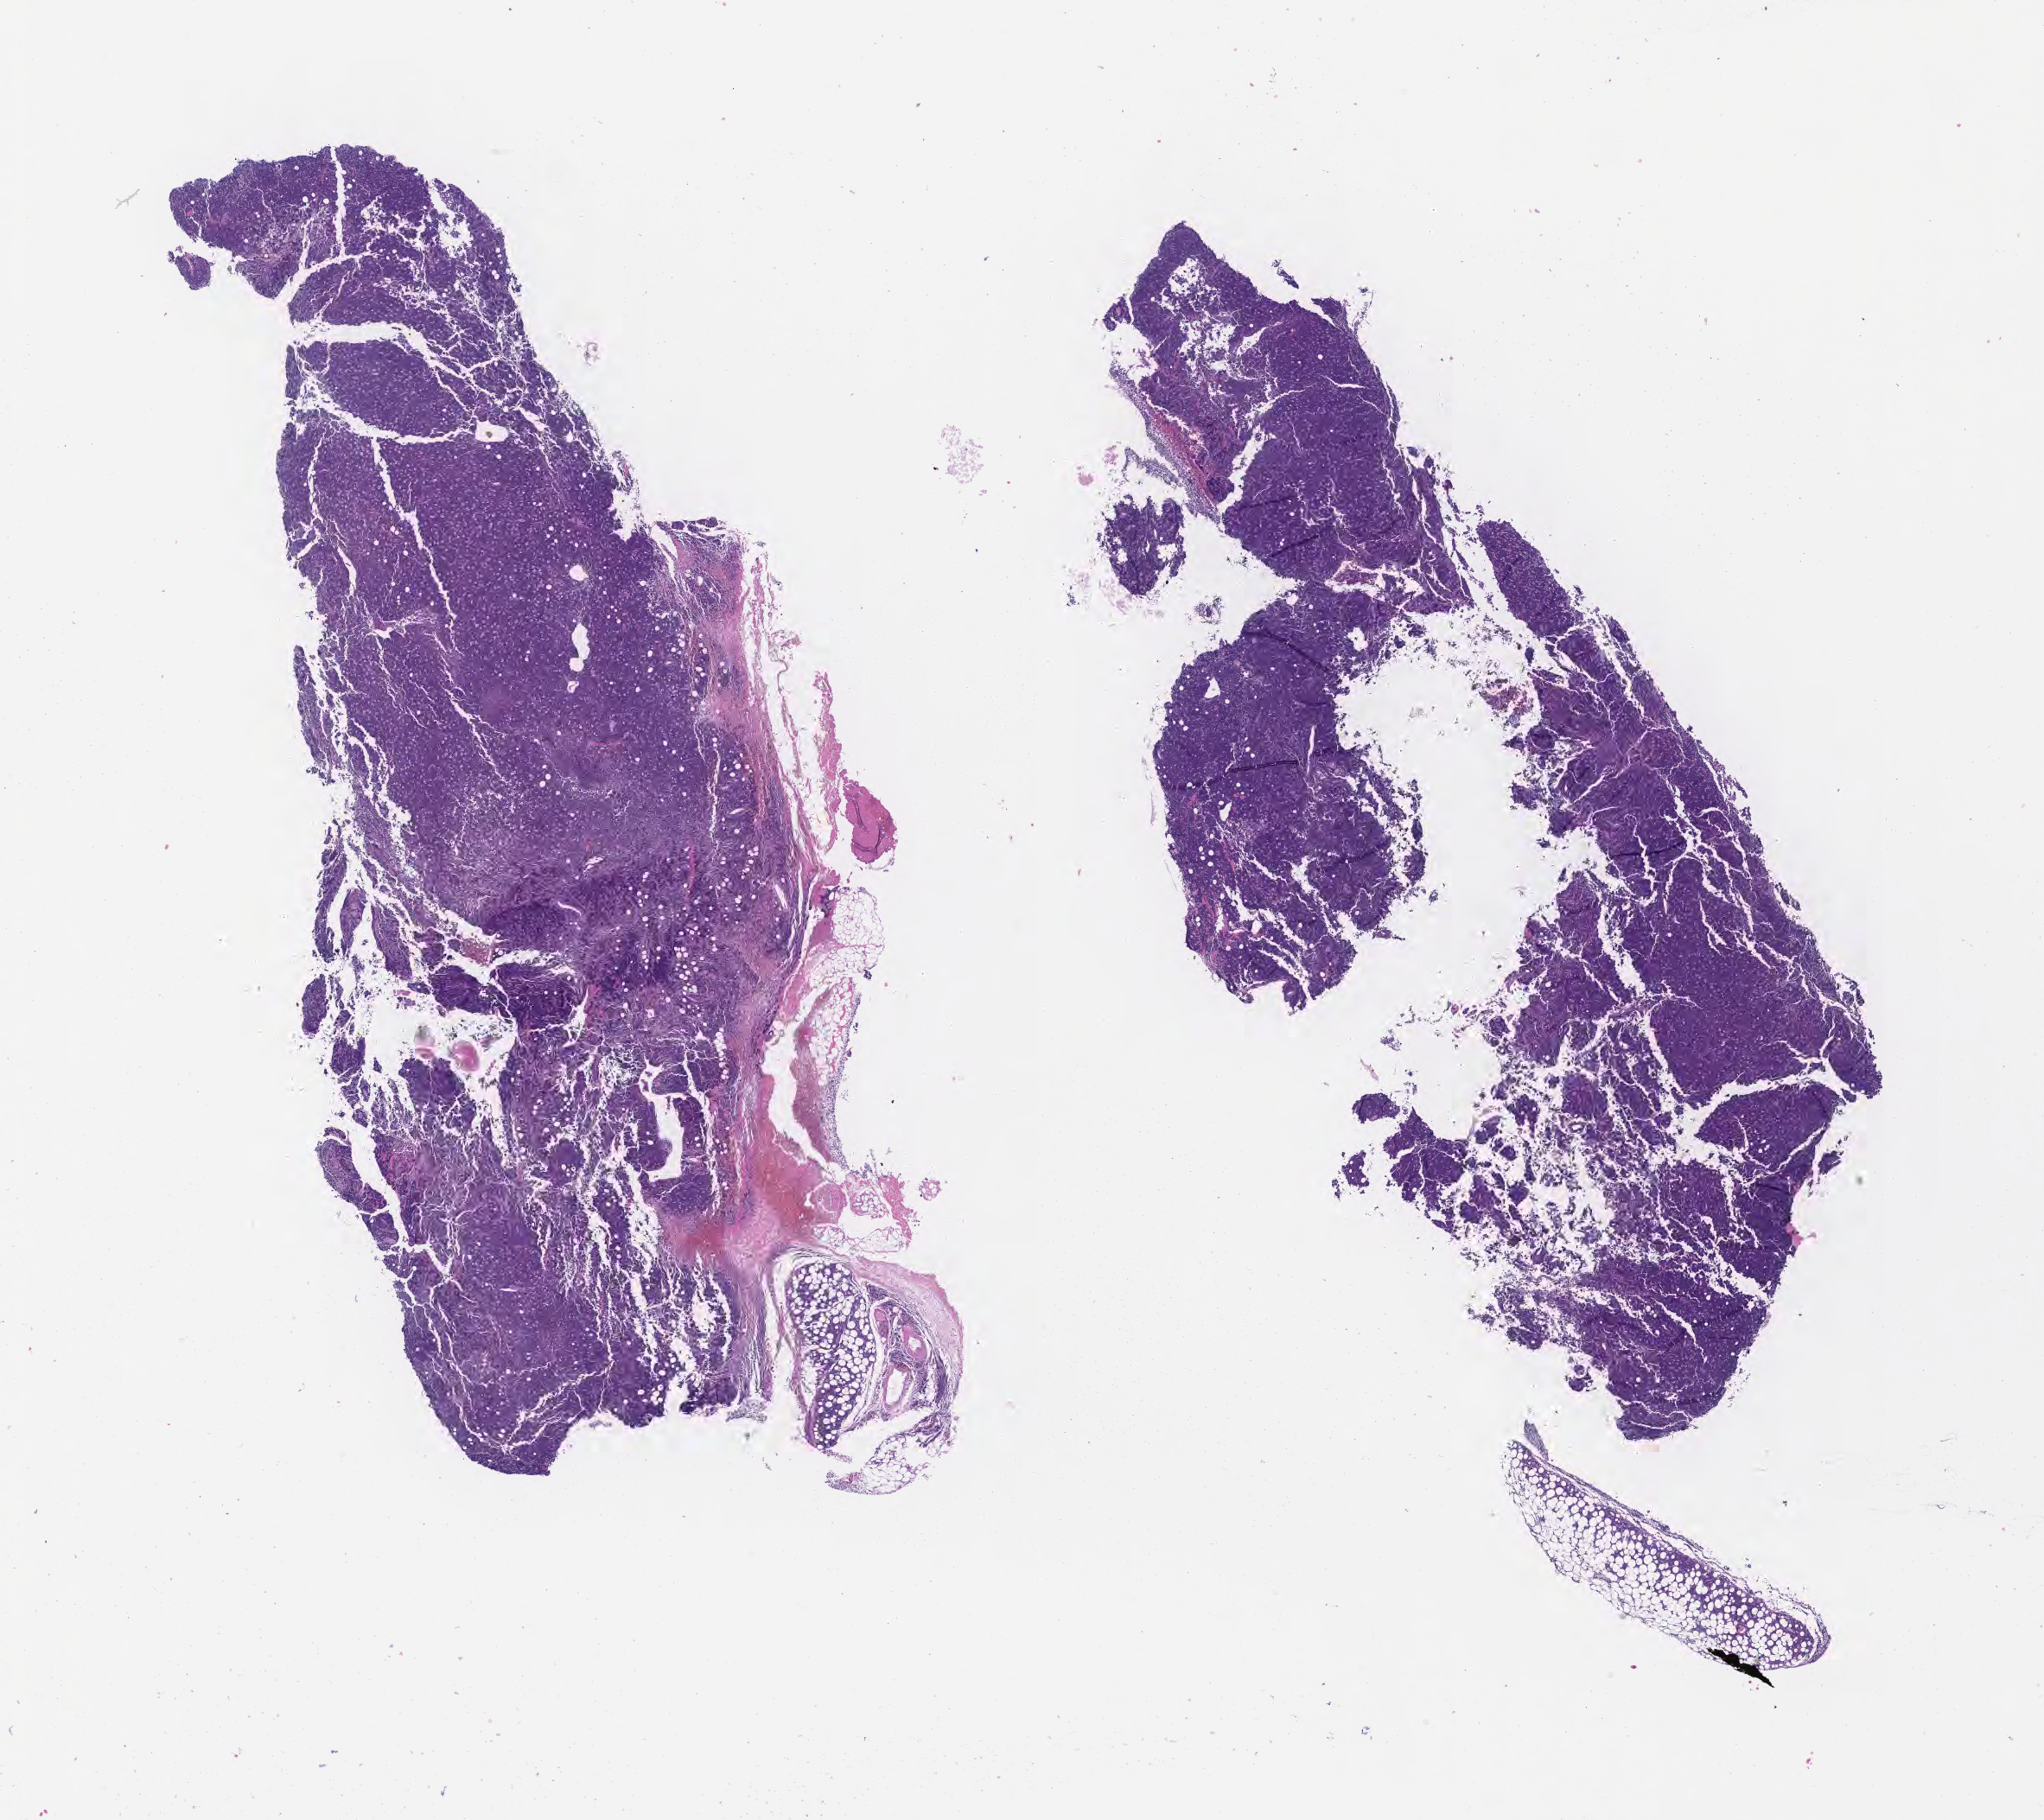
Digitized H&E-stained section, a low-resolution overview of the entire scanned area, about 19.1 x 17.0 mm. Specimen: tumor tissue. Patient female; age 16 years.
* diagnosis: Burkitt lymphoma, NOS